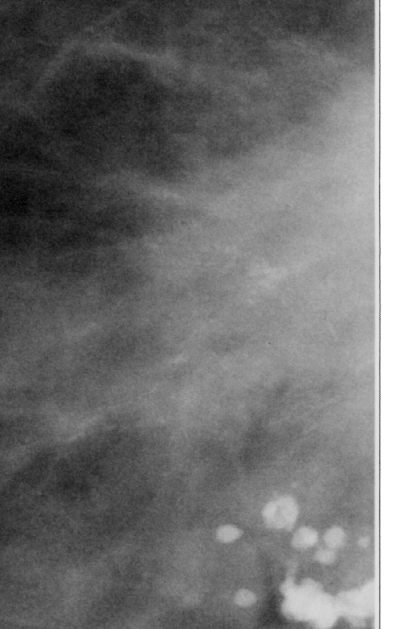
Crop from a digitized film mammogram around one marked abnormality; right breast; CC view.
Finding: mass, shape irregular / architectural distortion, margins ill defined / spiculated; BI-RADS assessment category 5; pathology result (as recorded, not read from the image): malignant.